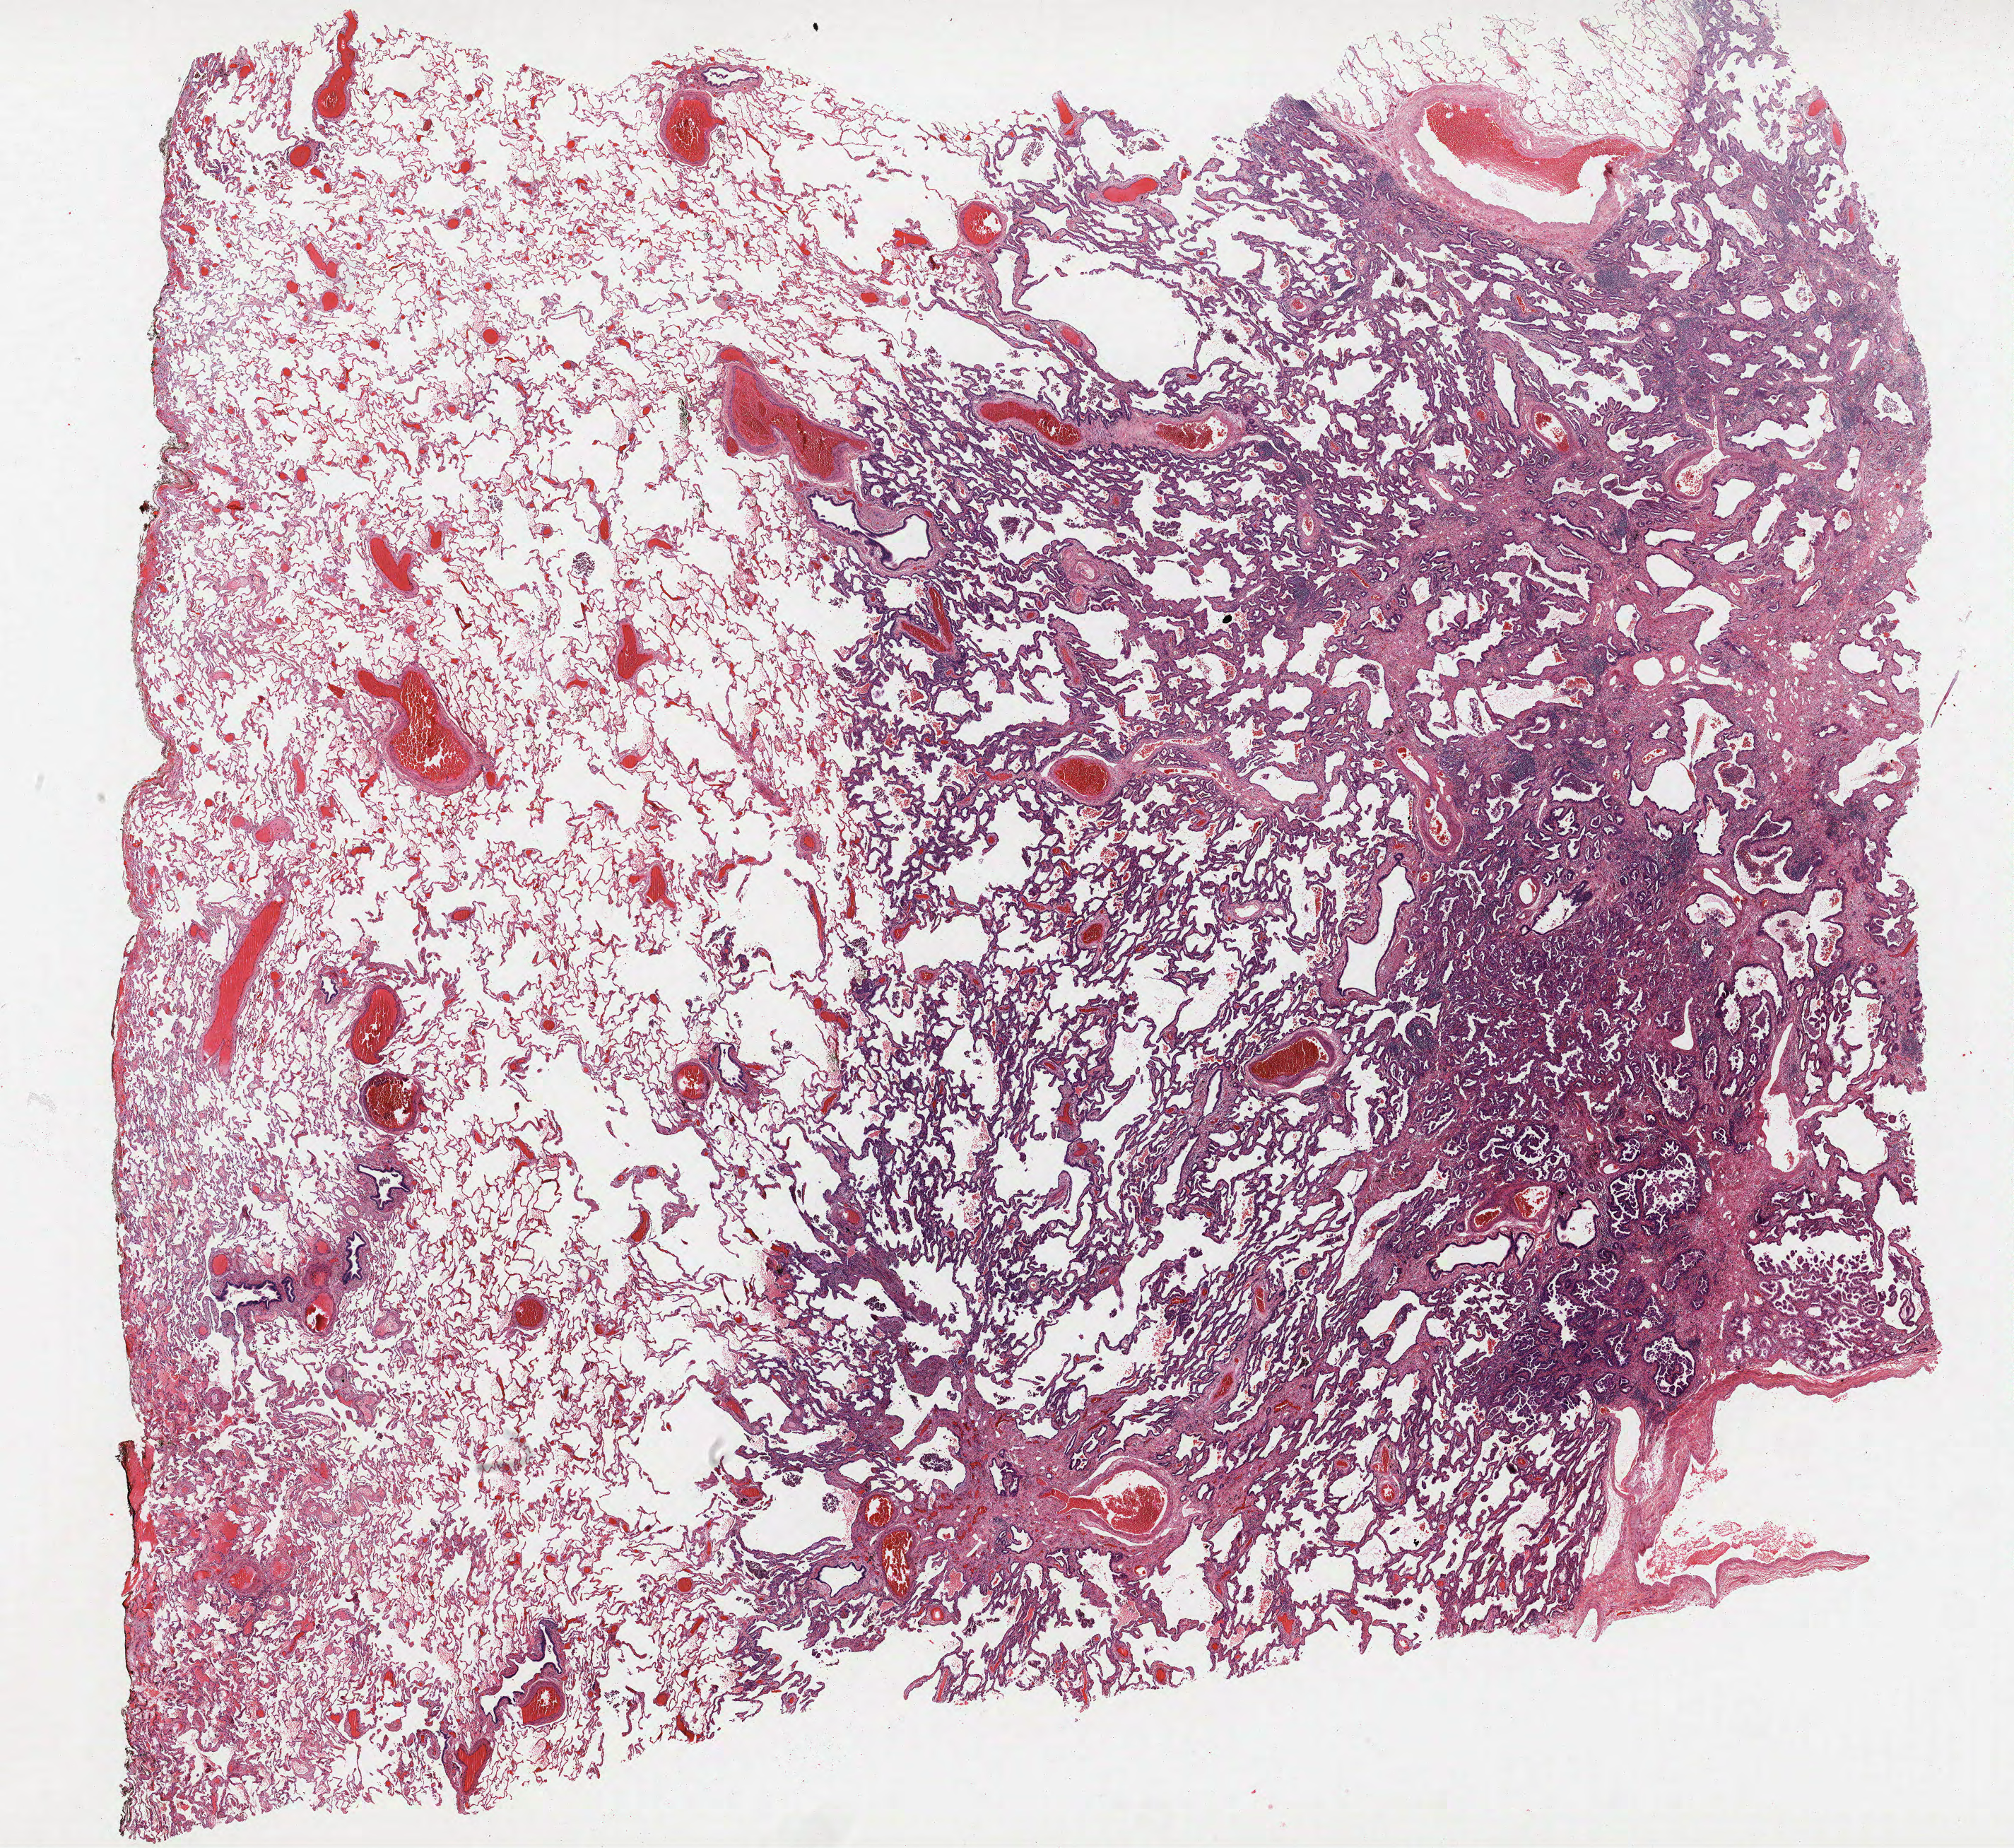
H&E whole-slide image, a low-resolution overview of the entire scanned area, about 22.8 x 20.9 mm (acquisition: 40x scan). Formalin-fixed paraffin-embedded (FFPE) section. Lung. Female, age 65 at enrolment. Former smoker at enrolment.
Participant's lung-cancer diagnosis: Adenocarcinoma, NOS (ICD-O-3 8140/3).